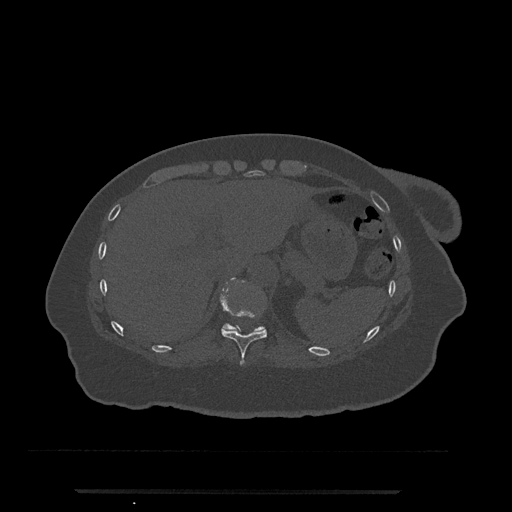
CT including the spine, one axial slice; position 269 of 797 along the scan axis; reconstruction kernel Br40s/3; bone window (W 1800 / L 400 HU); 512 × 512 image matrix. Patient: female, 51 years. From the clinical record (not read from this slice): primary cancer: neuro.
Outlined on this slice (semi-automatically segmented with operator editing):
- T10 vertebra: bounding box (x1, y1, x2, y2) in pixels: (220, 280, 267, 365)
- T11 vertebra: (223, 324, 263, 331)